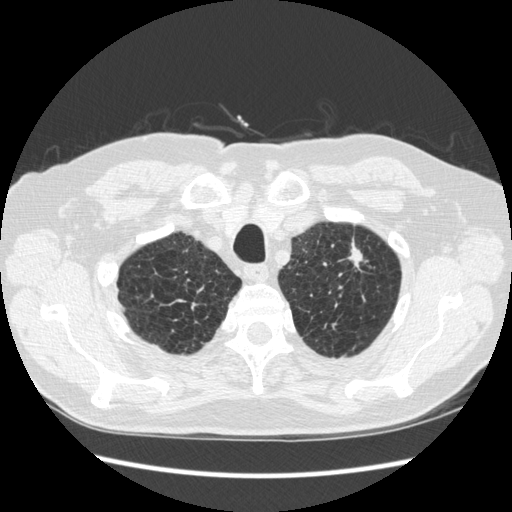
Low-dose screening chest CT, one axial slice. Position 234 of 267 along the scan axis. Reconstruction kernel STANDARD. 120 kVp. Lung window (W 1500 / L -600 HU). 1.25 mm slice thickness. 512 × 512 image matrix.
Outlined on this slice (outlined manually by an expert reader):
- lesion 1 (tumor, upper lobe of left lung): bounding box (x1, y1, x2, y2) in pixels: (348, 242, 362, 269)